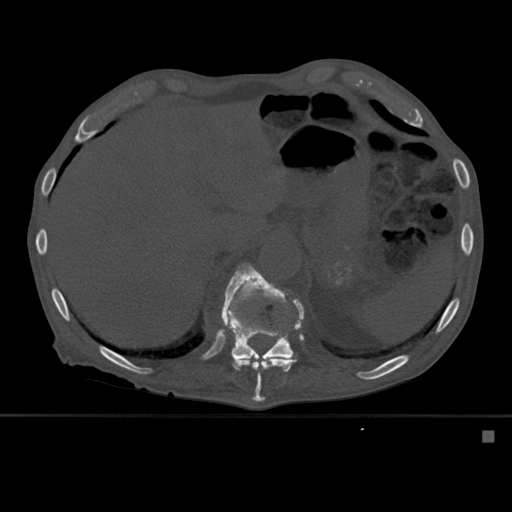
CT including the spine, one axial slice. Position 285 of 527 along the scan axis. Bone window (W 1800 / L 400 HU). 1.5 mm slice thickness. 512 × 512 image matrix, field of view 373 × 373 mm. Patient: male, 78 years. Case-level facts recorded for this patient, not image findings: primary cancer: prostate.
Outlined on this slice (semi-automatic segmentation, software-assisted and operator-edited):
- T11 vertebra: box from (x=231, y=262) to (x=301, y=402) px
- T12 vertebra: (x=221, y=274)–(x=304, y=359)